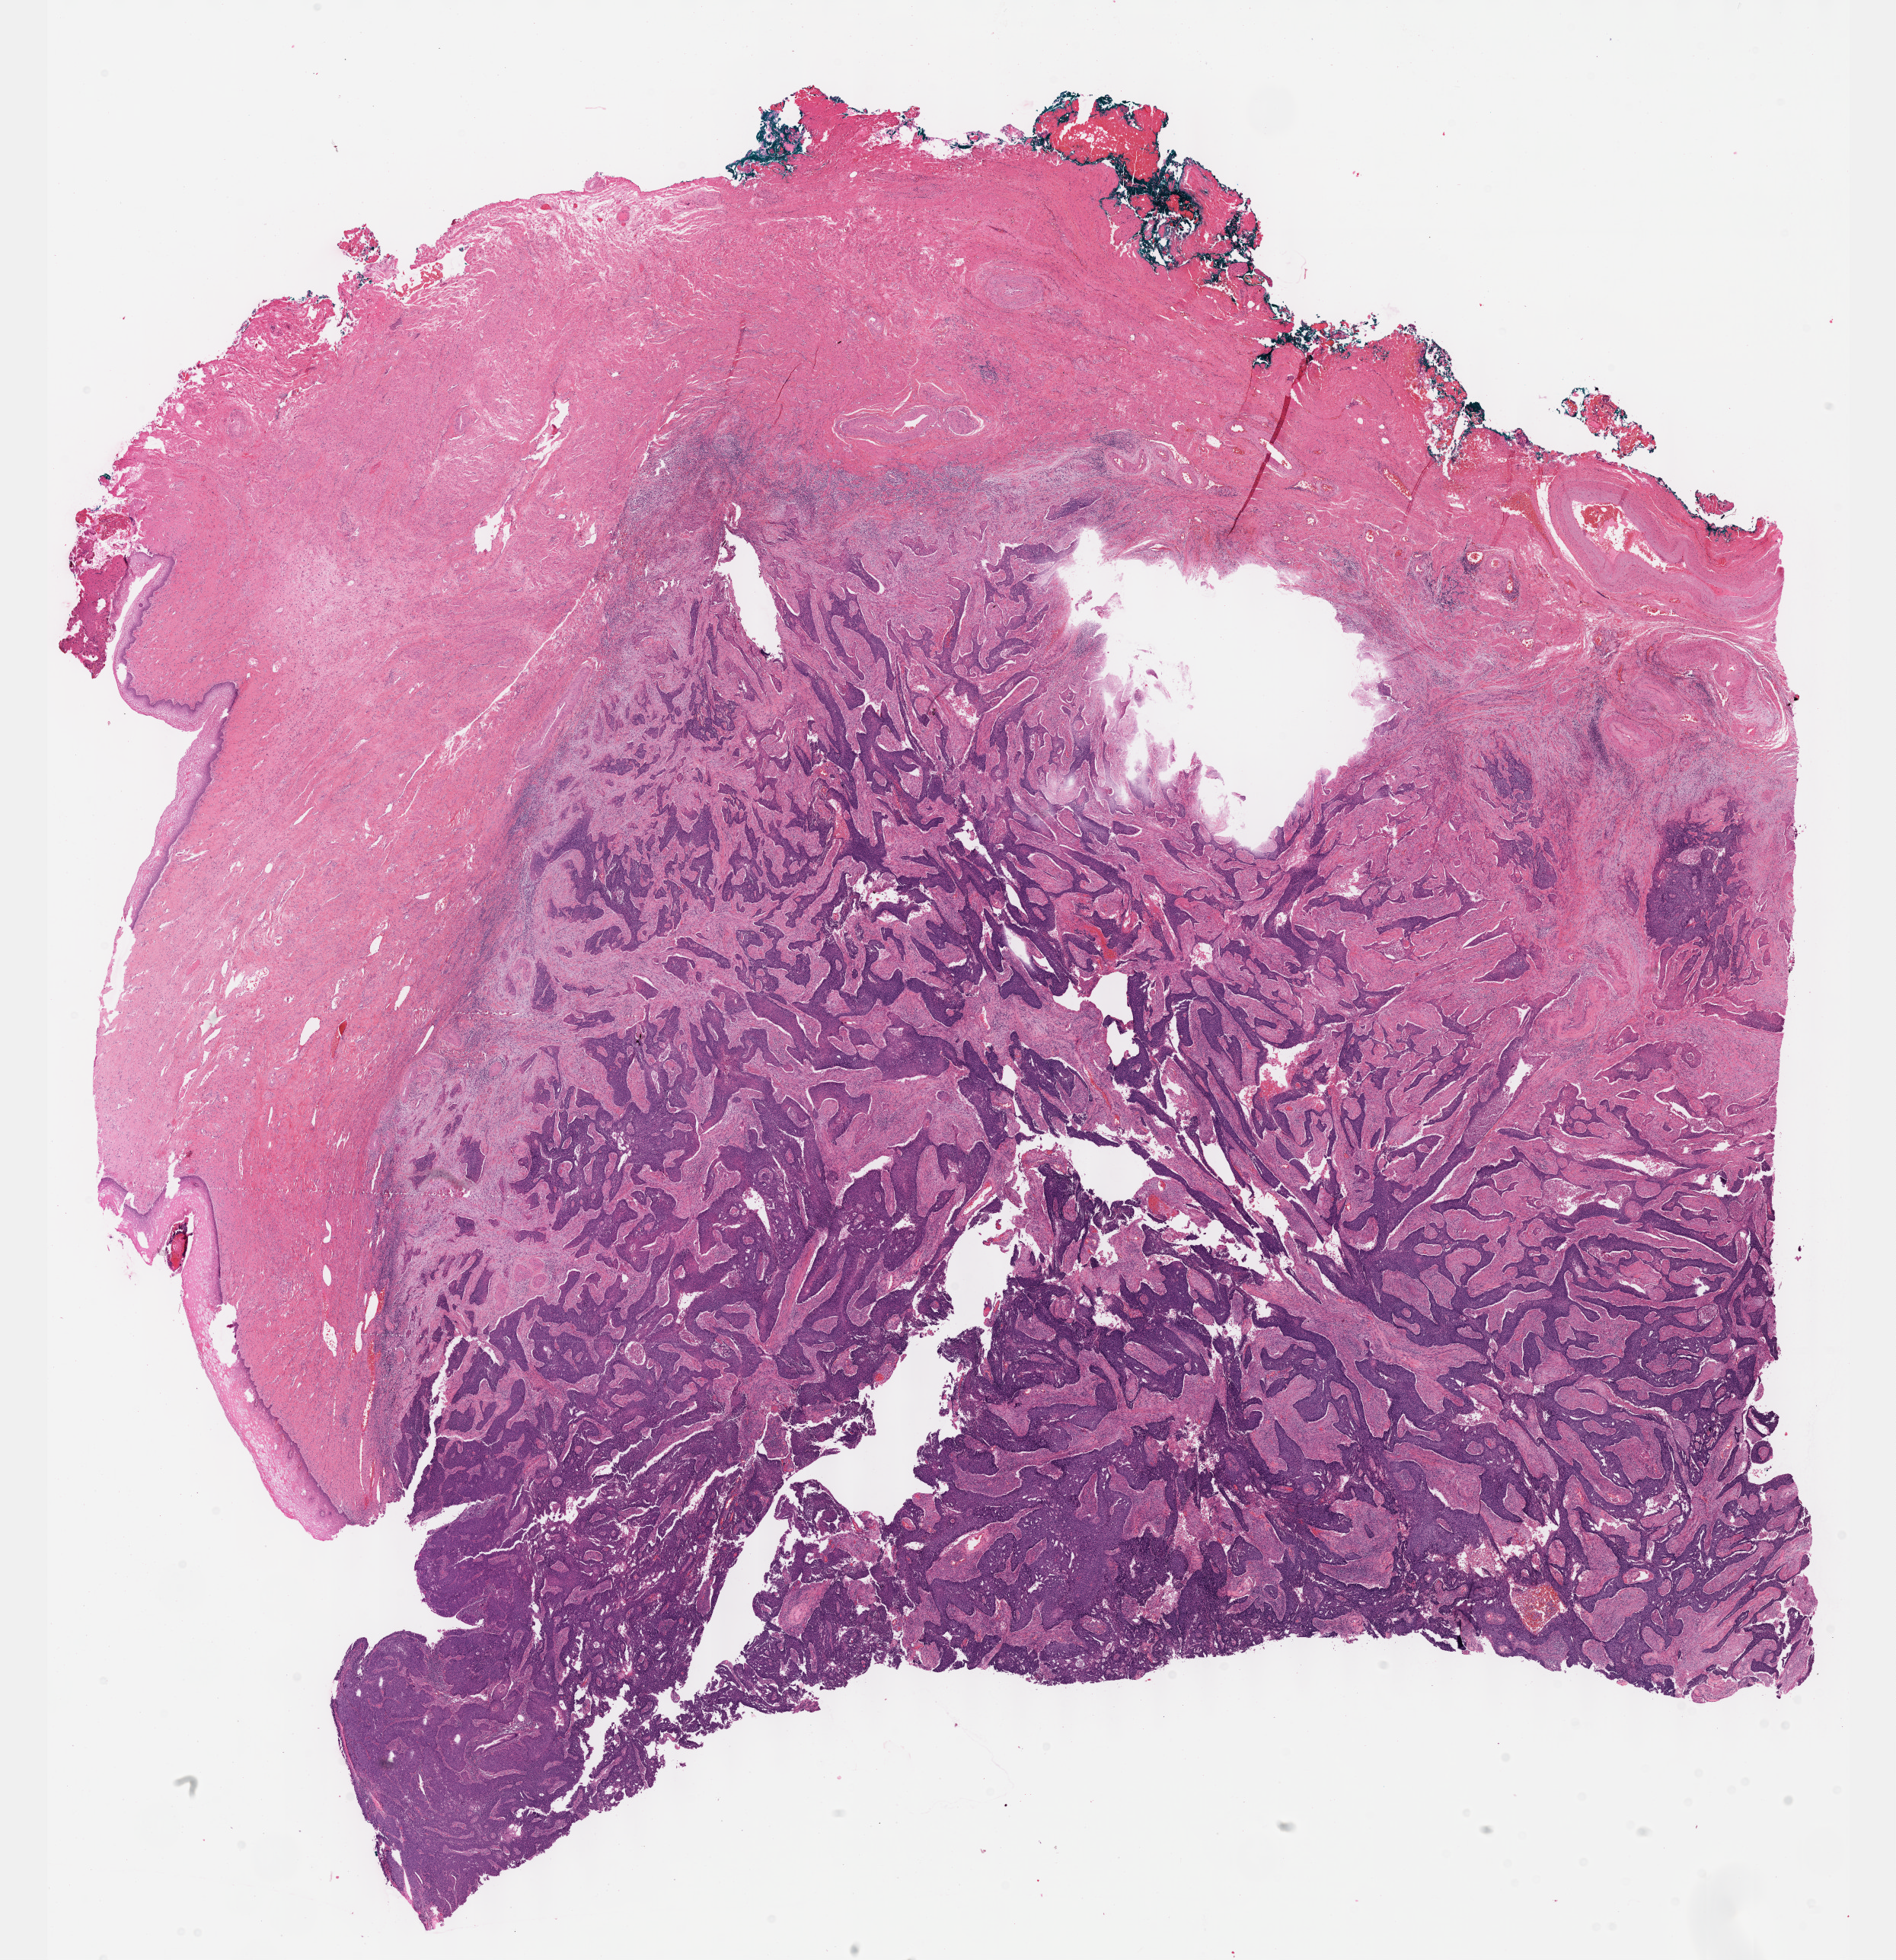
Whole-slide histology image, H&E-stained, a low-resolution overview of the entire scanned area, about 20.1 x 20.8 mm (slide scanned at 40x), formalin-fixed paraffin-embedded (FFPE) diagnostic section, primary tumour sample from the cervix. Patient: female, age at initial diagnosis 62 years.
Histologic diagnosis: Squamous cell carcinoma, NOS.